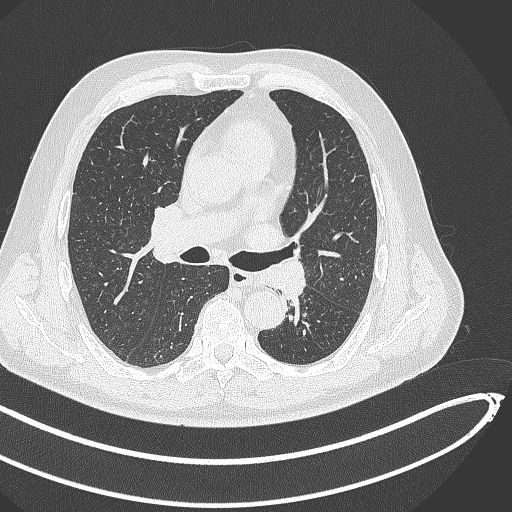
Chest CT, one axial slice. Position 272 of 468 along the scan axis. 120 kVp. Lung window (W 1500 / L -600 HU). 512 × 512 image matrix, field of view 400 × 400 mm. Male patient, age 64 years. Case-level facts recorded for this patient, not image findings: clinical TNM (as recorded): T1c N0 M0; histopathological grade: G2.
Structures marked on this image (rectangle marked by the reading radiologist):
- lung tumour (recorded histology: squamous cell carcinoma): bounding box <262,257,312,305> (left, top, right, bottom; pixels)